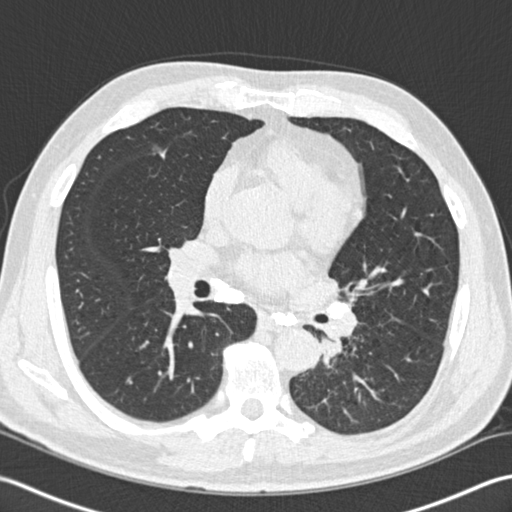
Low-dose screening chest CT, one axial slice; slice 92 of 170 in the series (ordered by position); reconstruction kernel B30f; 120 kVp; lung window (W 1500 / L -600 HU); 2 mm slice thickness; 512 × 512 image matrix.
Structures marked on this image (manually delineated by an expert):
- lesion 1 (tumor, lower lobe of left lung): bounding box (x1, y1, x2, y2) in pixels: (320, 337, 342, 361)